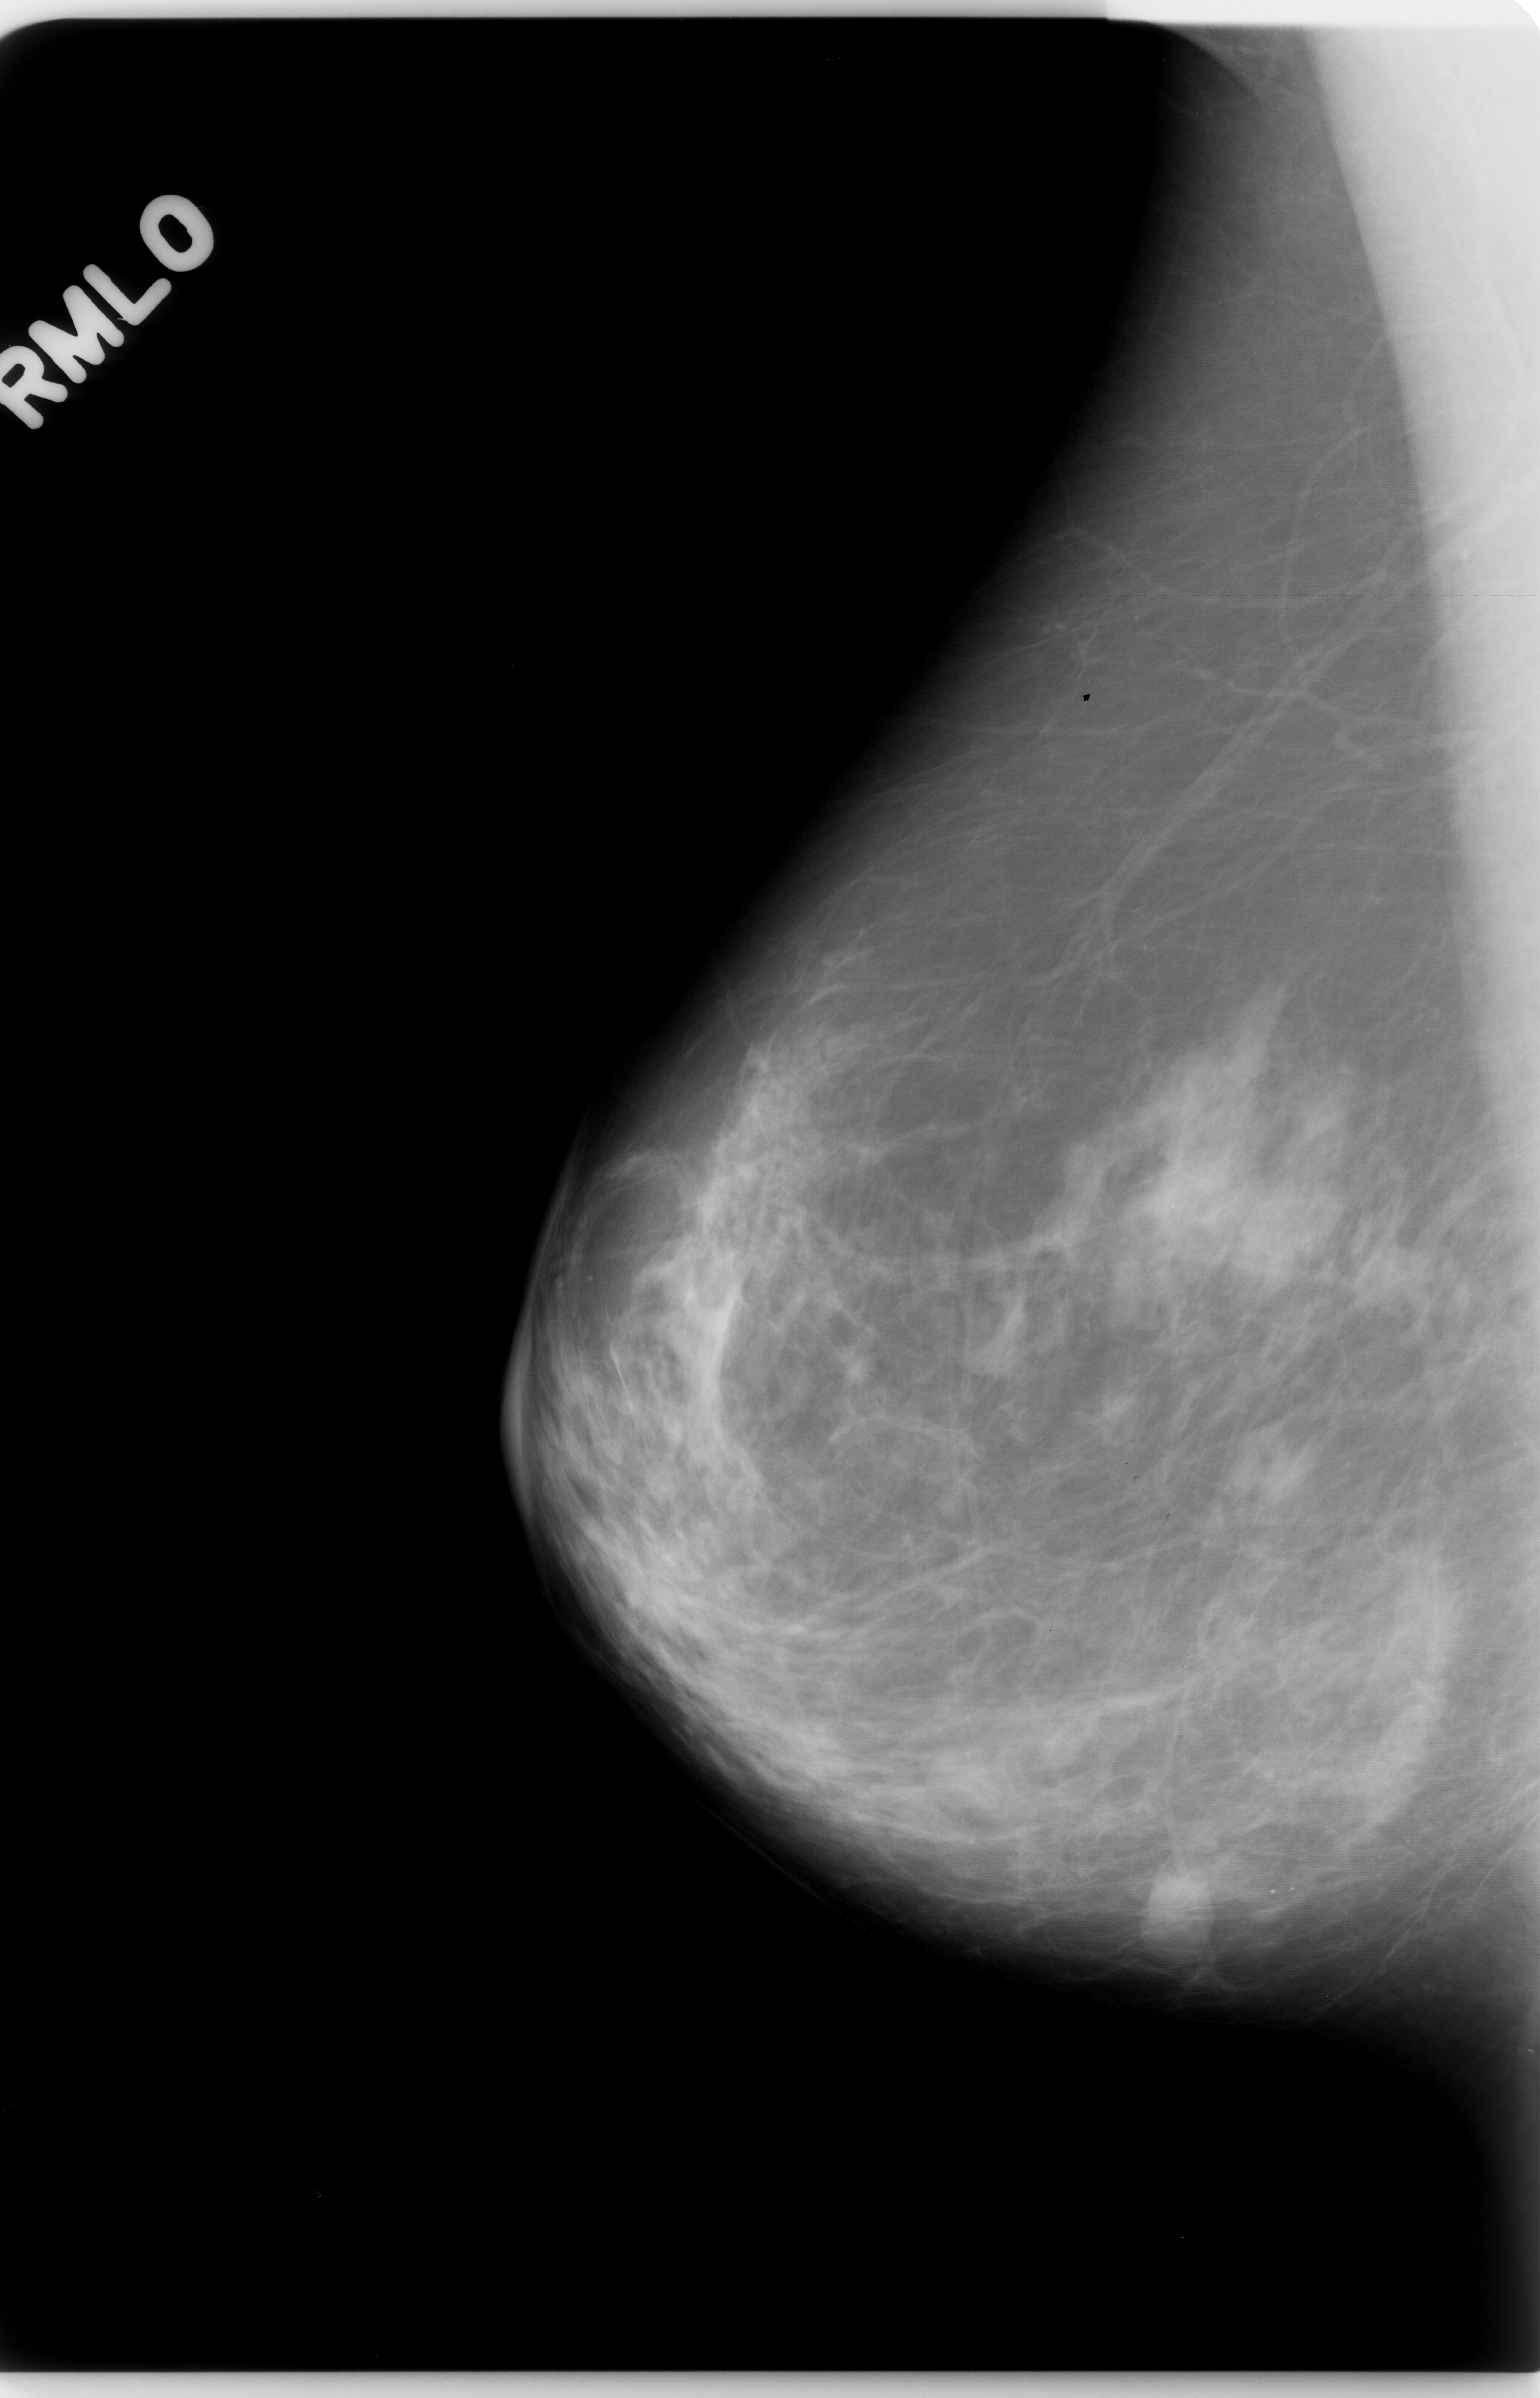
Digitized screen-film mammogram, right breast, mediolateral oblique (MLO) view, breast composition: scattered fibroglandular densities (BI-RADS density category 2 of 4).
- Marked findings (only marked abnormalities are described; nothing is implied about the rest of the image): mass, shape oval, margins circumscribed; BI-RADS assessment category 4; pathology result (as recorded, not read from the image): benign.